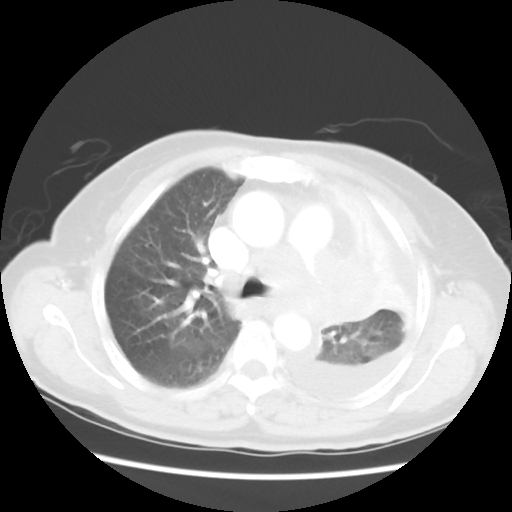
Chest CT, one axial slice. Slice 36 of 52 in the series (ordered by position). Reconstruction kernel STANDARD. Lung window (W 1500 / L -600 HU). 5 mm slice thickness. 512 × 512 image matrix. Female patient, age 72 years. From the clinical record (not read from this slice): clinical TNM (as recorded): T4 N3 M1b; histopathological grade: G3.
Outlined on this slice (bounding box drawn by a radiologist):
- lung tumour (recorded histology: large cell carcinoma): bounding box <295,243,390,339> (left, top, right, bottom; pixels)